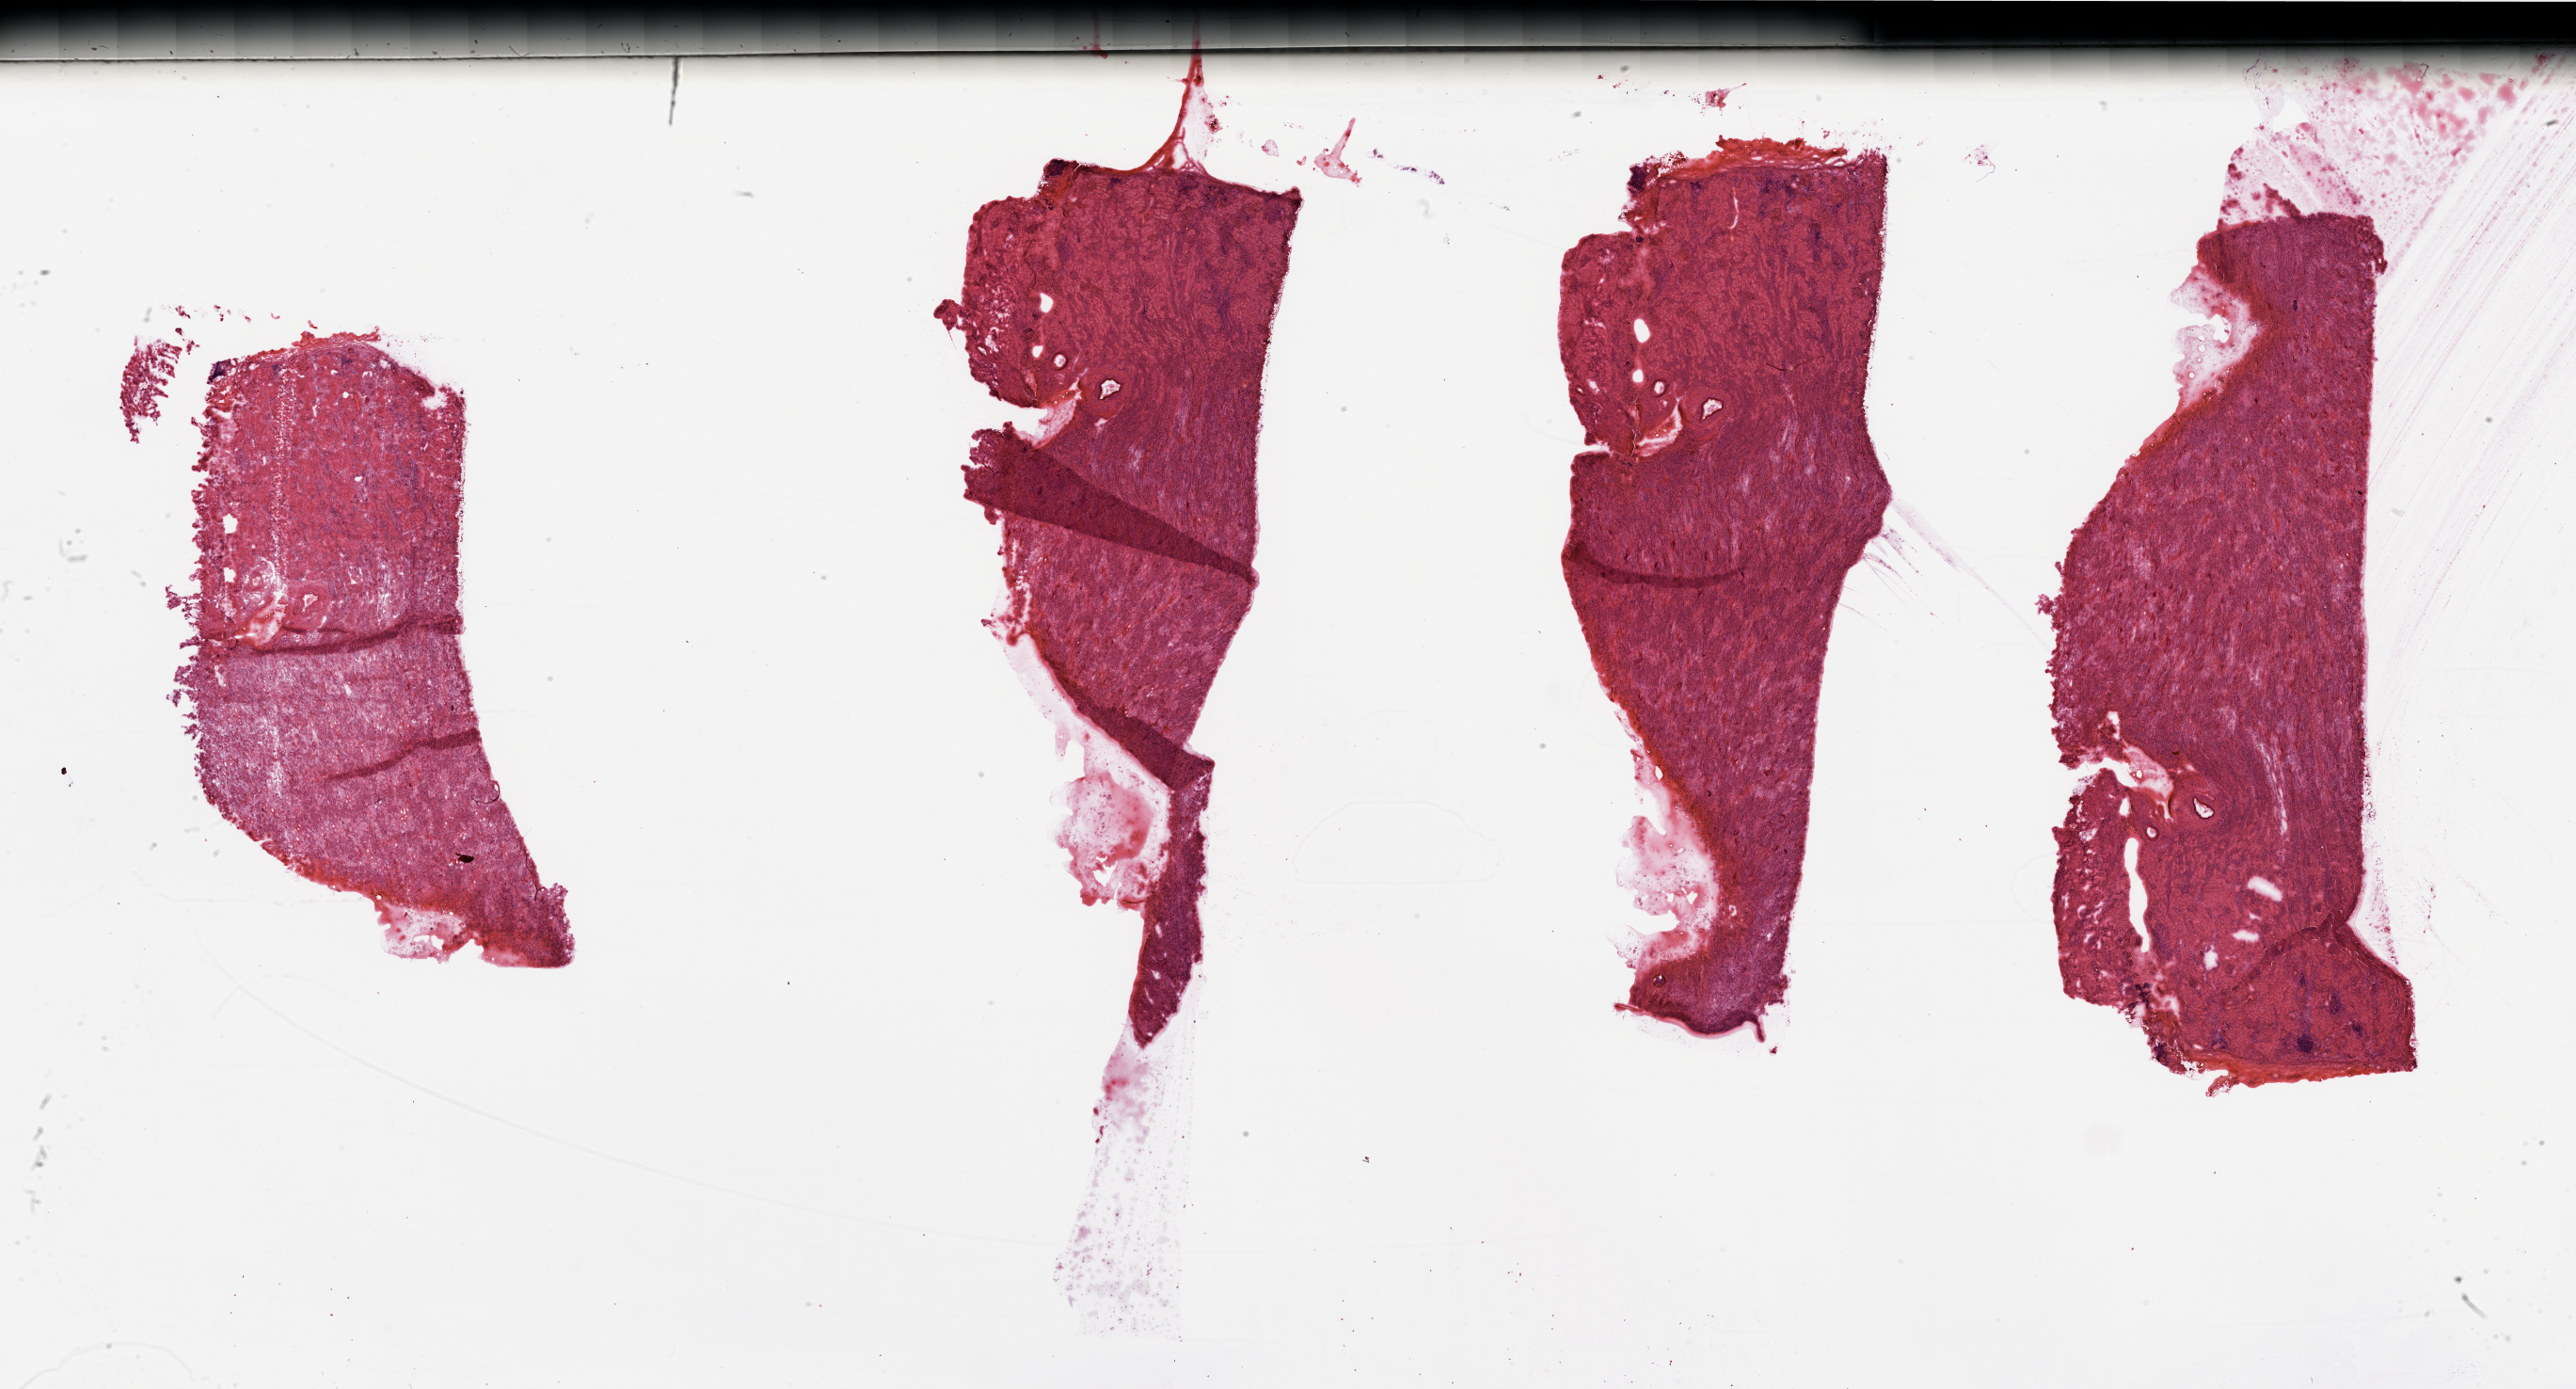
Whole-slide histology image, Hematoxylin and eosin (H&E) stained — a low-resolution overview of the entire scanned area, about 43.3 x 23.4 mm, normal (non-tumour) tissue sample, sampled site: kidney. Male, 84 y/o.
This section: normal (non-tumour) tissue from the same patient. Patient diagnosis: Renal cell carcinoma, NOS.